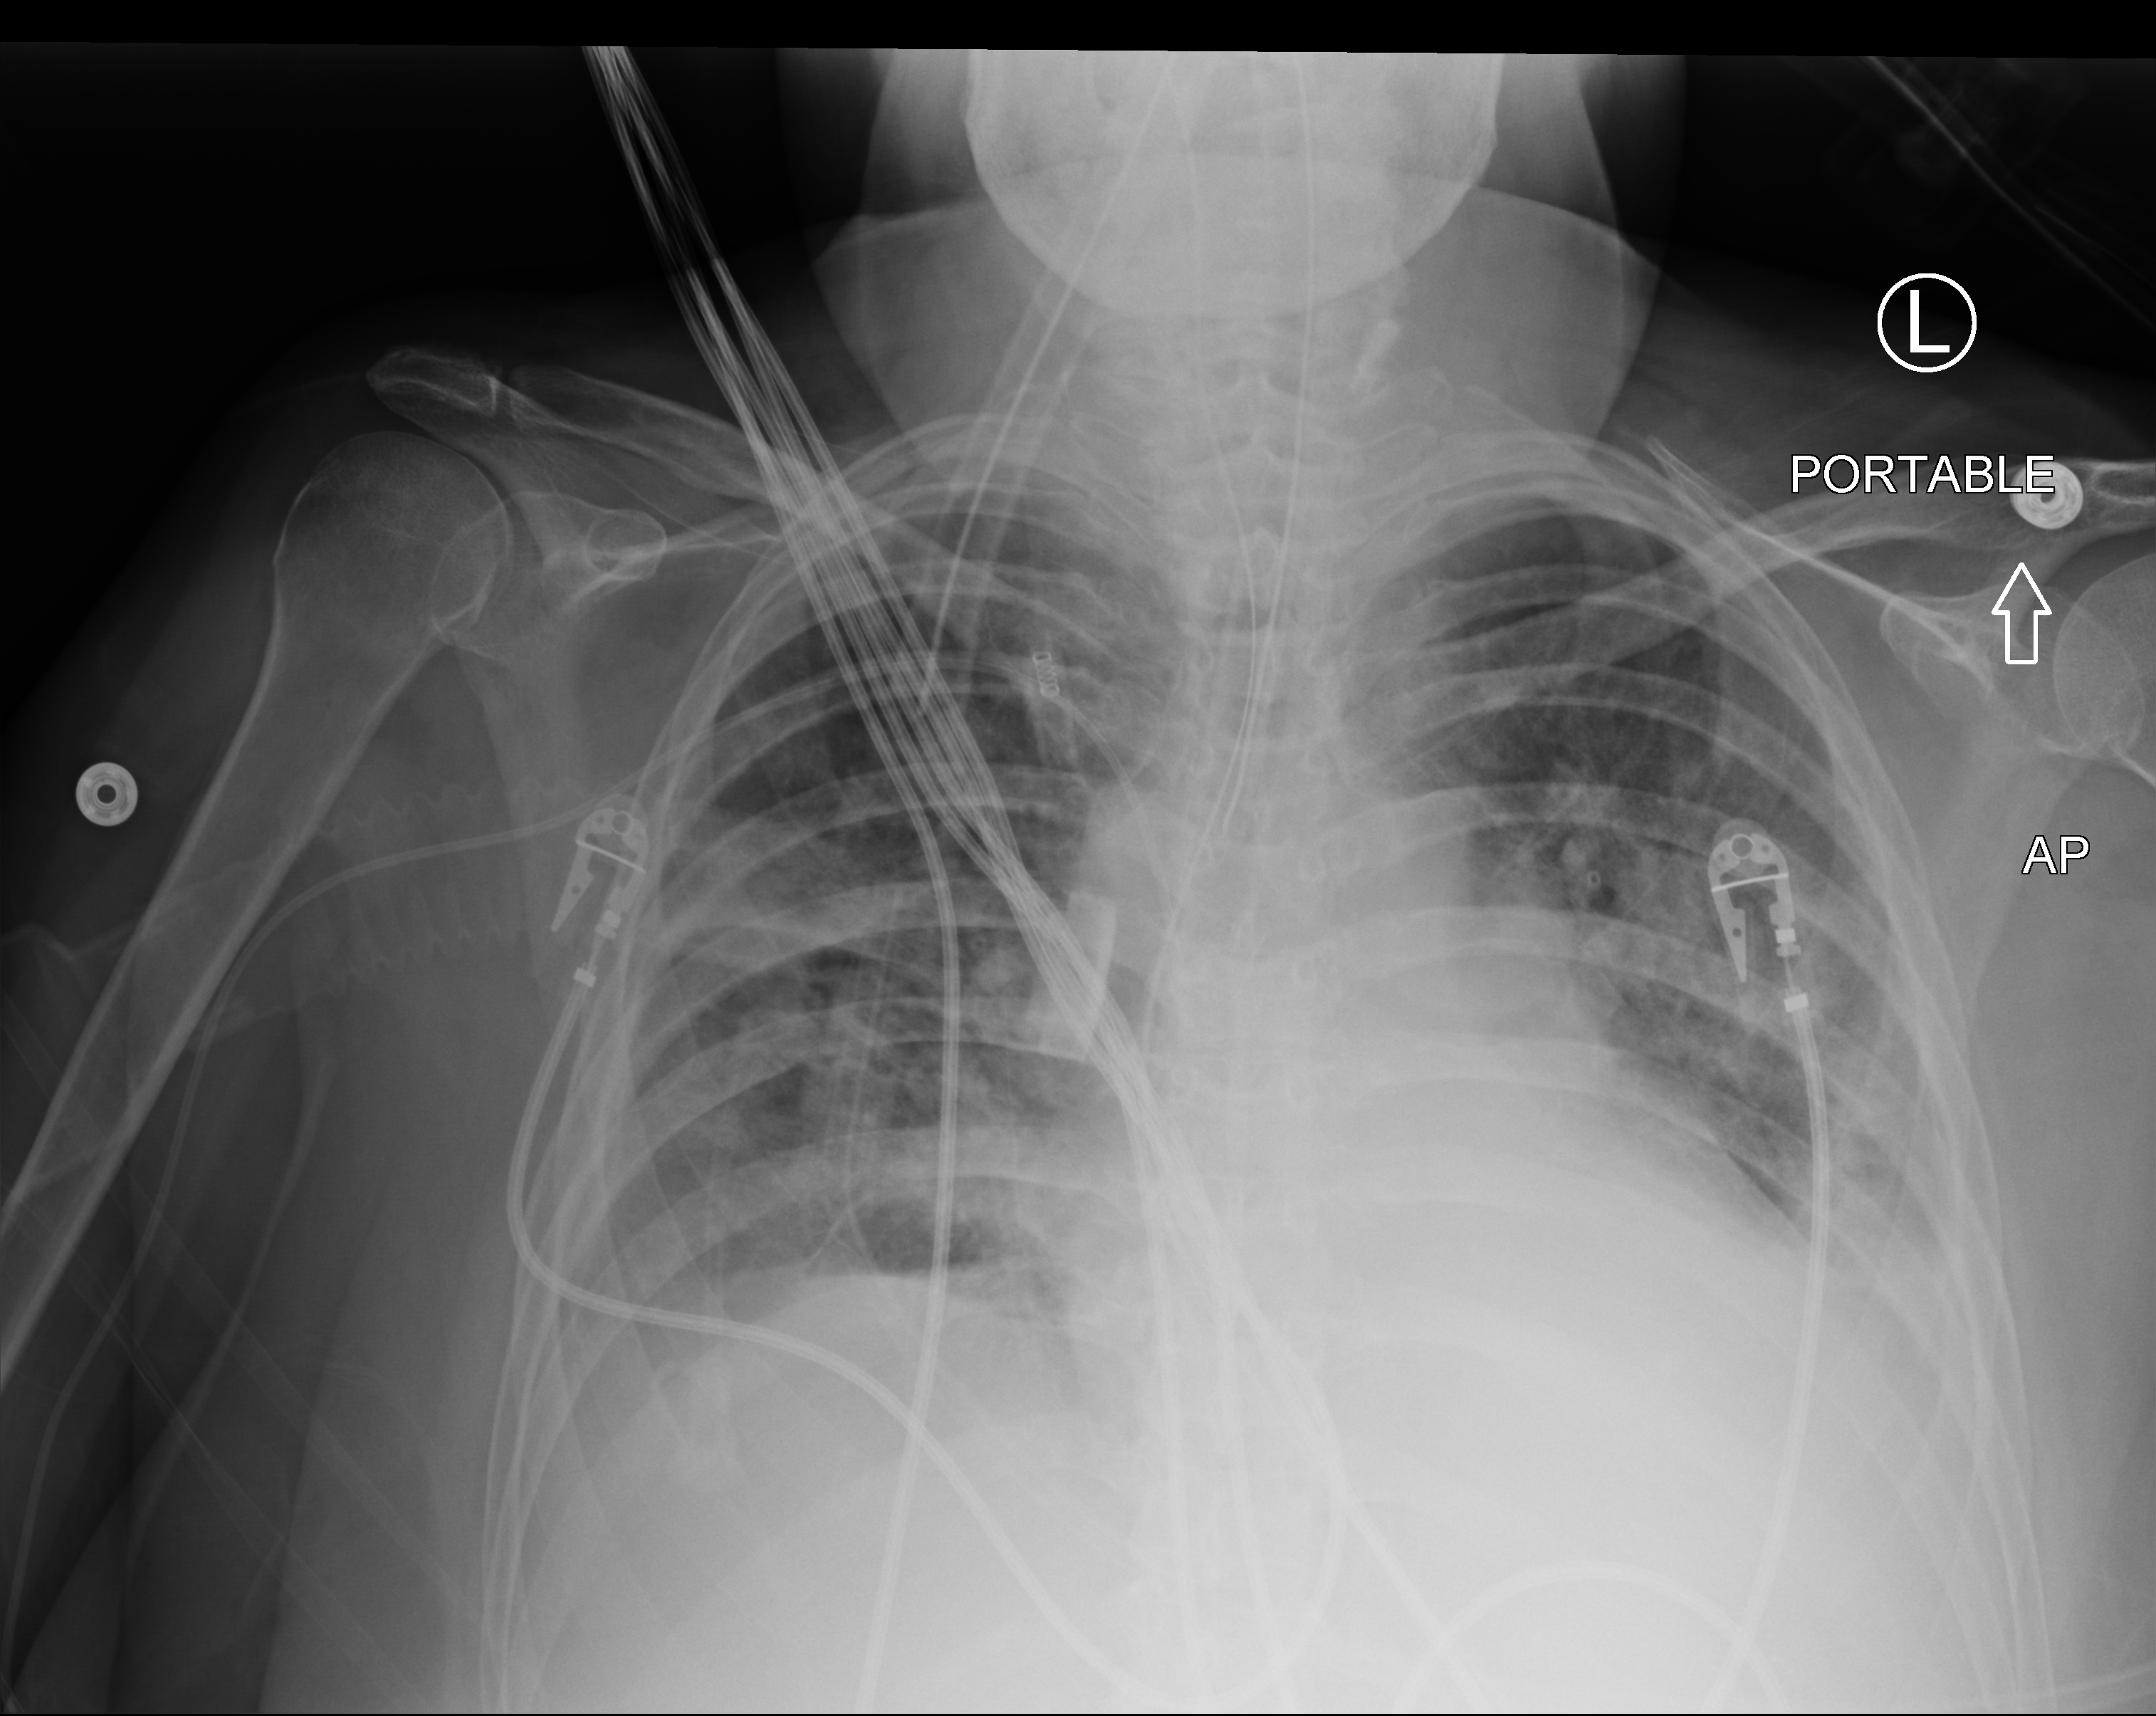
Chest X-ray (portable); anteroposterior (AP) projection. Patient hospitalised with COVID-19; female, aged 60–74 years.
Admission-level facts for this patient (not findings on this image; timing relative to this image not recorded):
- mechanically ventilated during this hospital stay: yes
- length of hospital stay: 9 days